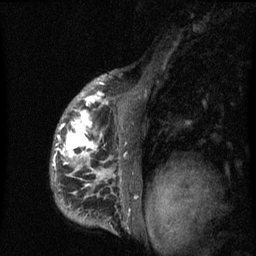
Breast MRI (dynamic contrast-enhanced), one sagittal slice. Position 47 of 60 along the scan axis. Dynamic contrast-enhanced series, image 2 of 3 at this slice position (ordered by acquisition). 1.5 T. TE 4.2 ms, TR 8 ms. 2 mm slice thickness. 256 × 256 image matrix, field of view 190 × 190 mm. Patient: female, 50 years.
Outlined on this slice (semi-automatic segmentation, software-assisted and operator-edited):
- analysis volume of interest (the breast-tissue region the enhancement analysis was run in; not a lesion): bounding box <50,90,142,216> (left, top, right, bottom; pixels)
- tumour enhancement mask (voxels above the 70 % enhancement threshold inside the analysis volume of interest): <52,91,121,186>